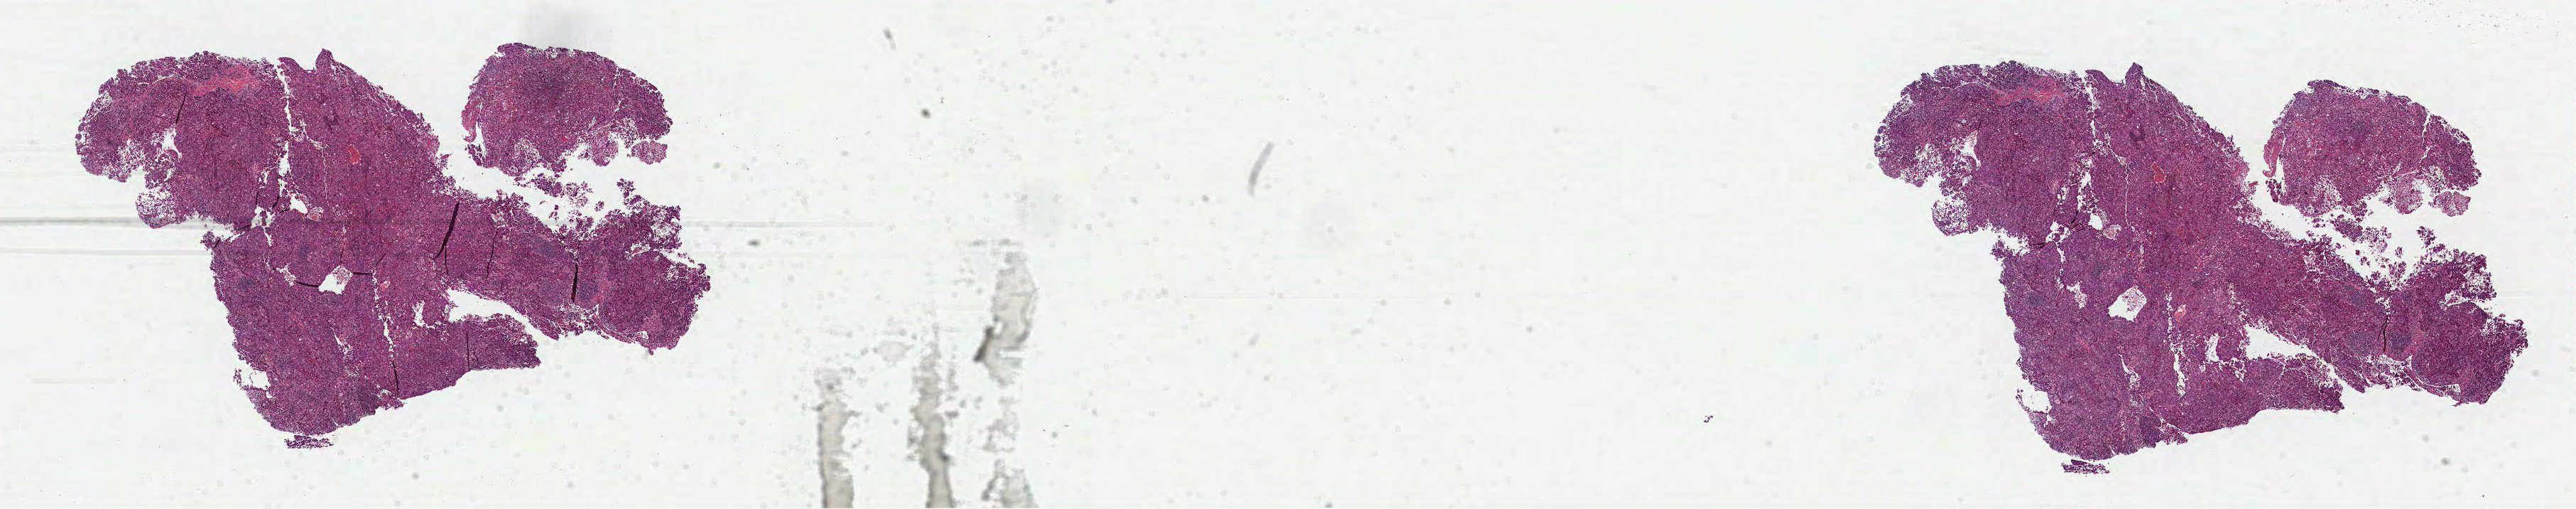
Whole-slide histology image, Hematoxylin and eosin (H&E) stained, a low-resolution overview of the entire scanned area, about 29.2 x 5.8 mm (slide scanned at 40x); FFPE section; lung, primary tumour sample. Female patient; age at initial diagnosis 33 years.
Histologic diagnosis: Adenocarcinoma, NOS (upper lobe, lung).